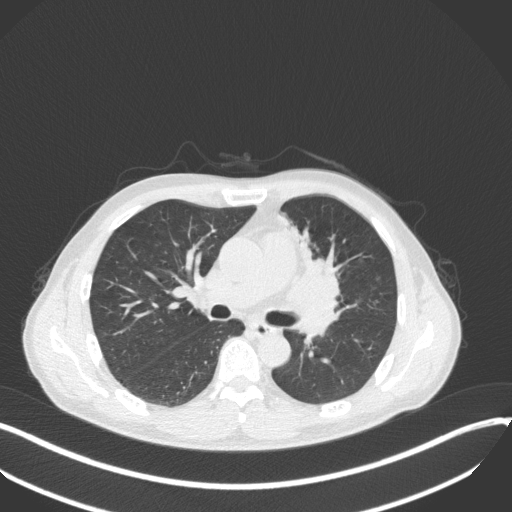
Chest CT, one axial slice. Slice 197 of 411 in the series (ordered by position). Reconstruction kernel B31f. Lung window (W 1500 / L -600 HU). 1 mm slice thickness. 512 × 512 image matrix. Patient: male, 56 years. From the clinical record (not read from this slice): clinical TNM (as recorded): T2a N0 M0.
Outlined on this slice (rectangle marked by the reading radiologist):
- lung tumour (recorded histology: squamous cell carcinoma): bounding box [x1, y1, x2, y2] px = [290, 235, 351, 311]